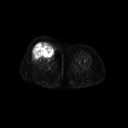
FDG PET of an extremity soft-tissue mass (from a PET/CT study), one axial slice. Position 35 of 267 along the scan axis. 128 × 128 image matrix. Female patient, age 56 years. Case-level facts recorded for this patient, not image findings: histological type: malignant solitary fibrous tumor; grade: intermediate; site of the primary tumour: right thigh.
Outlined on this slice (expert contour drawn on MRI and transferred to this co-registered scan by the dataset authors):
- gross tumour volume including surrounding oedema: bounding box [x1, y1, x2, y2] px = [33, 41, 55, 59]
- gross tumour volume (mass): [34, 41, 55, 58]